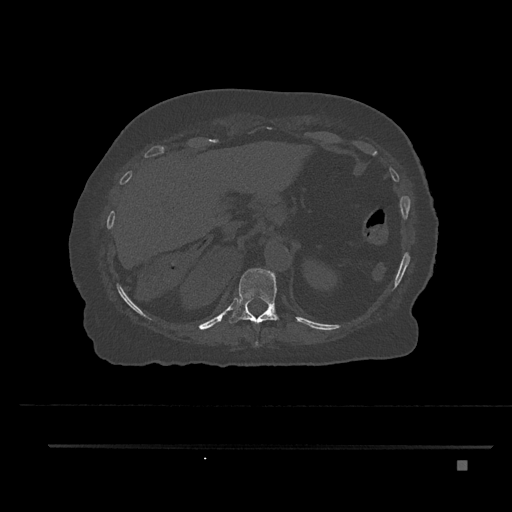
CT including the spine, one axial slice; 120 kVp; bone window (W 1800 / L 400 HU); 0.5 mm slice thickness; 512 × 512 image matrix, field of view 437 × 437 mm. Patient: female, 76 years. From the clinical record (not read from this slice): primary cancer: lung; vertebrae with lytic lesions (as recorded): T11, L3.
Annotated regions visible in this slice (semi-automatically segmented with operator editing):
- T10 vertebra: box from (x=254, y=340) to (x=259, y=347) px
- T11 vertebra: (x=229, y=268)–(x=280, y=325)